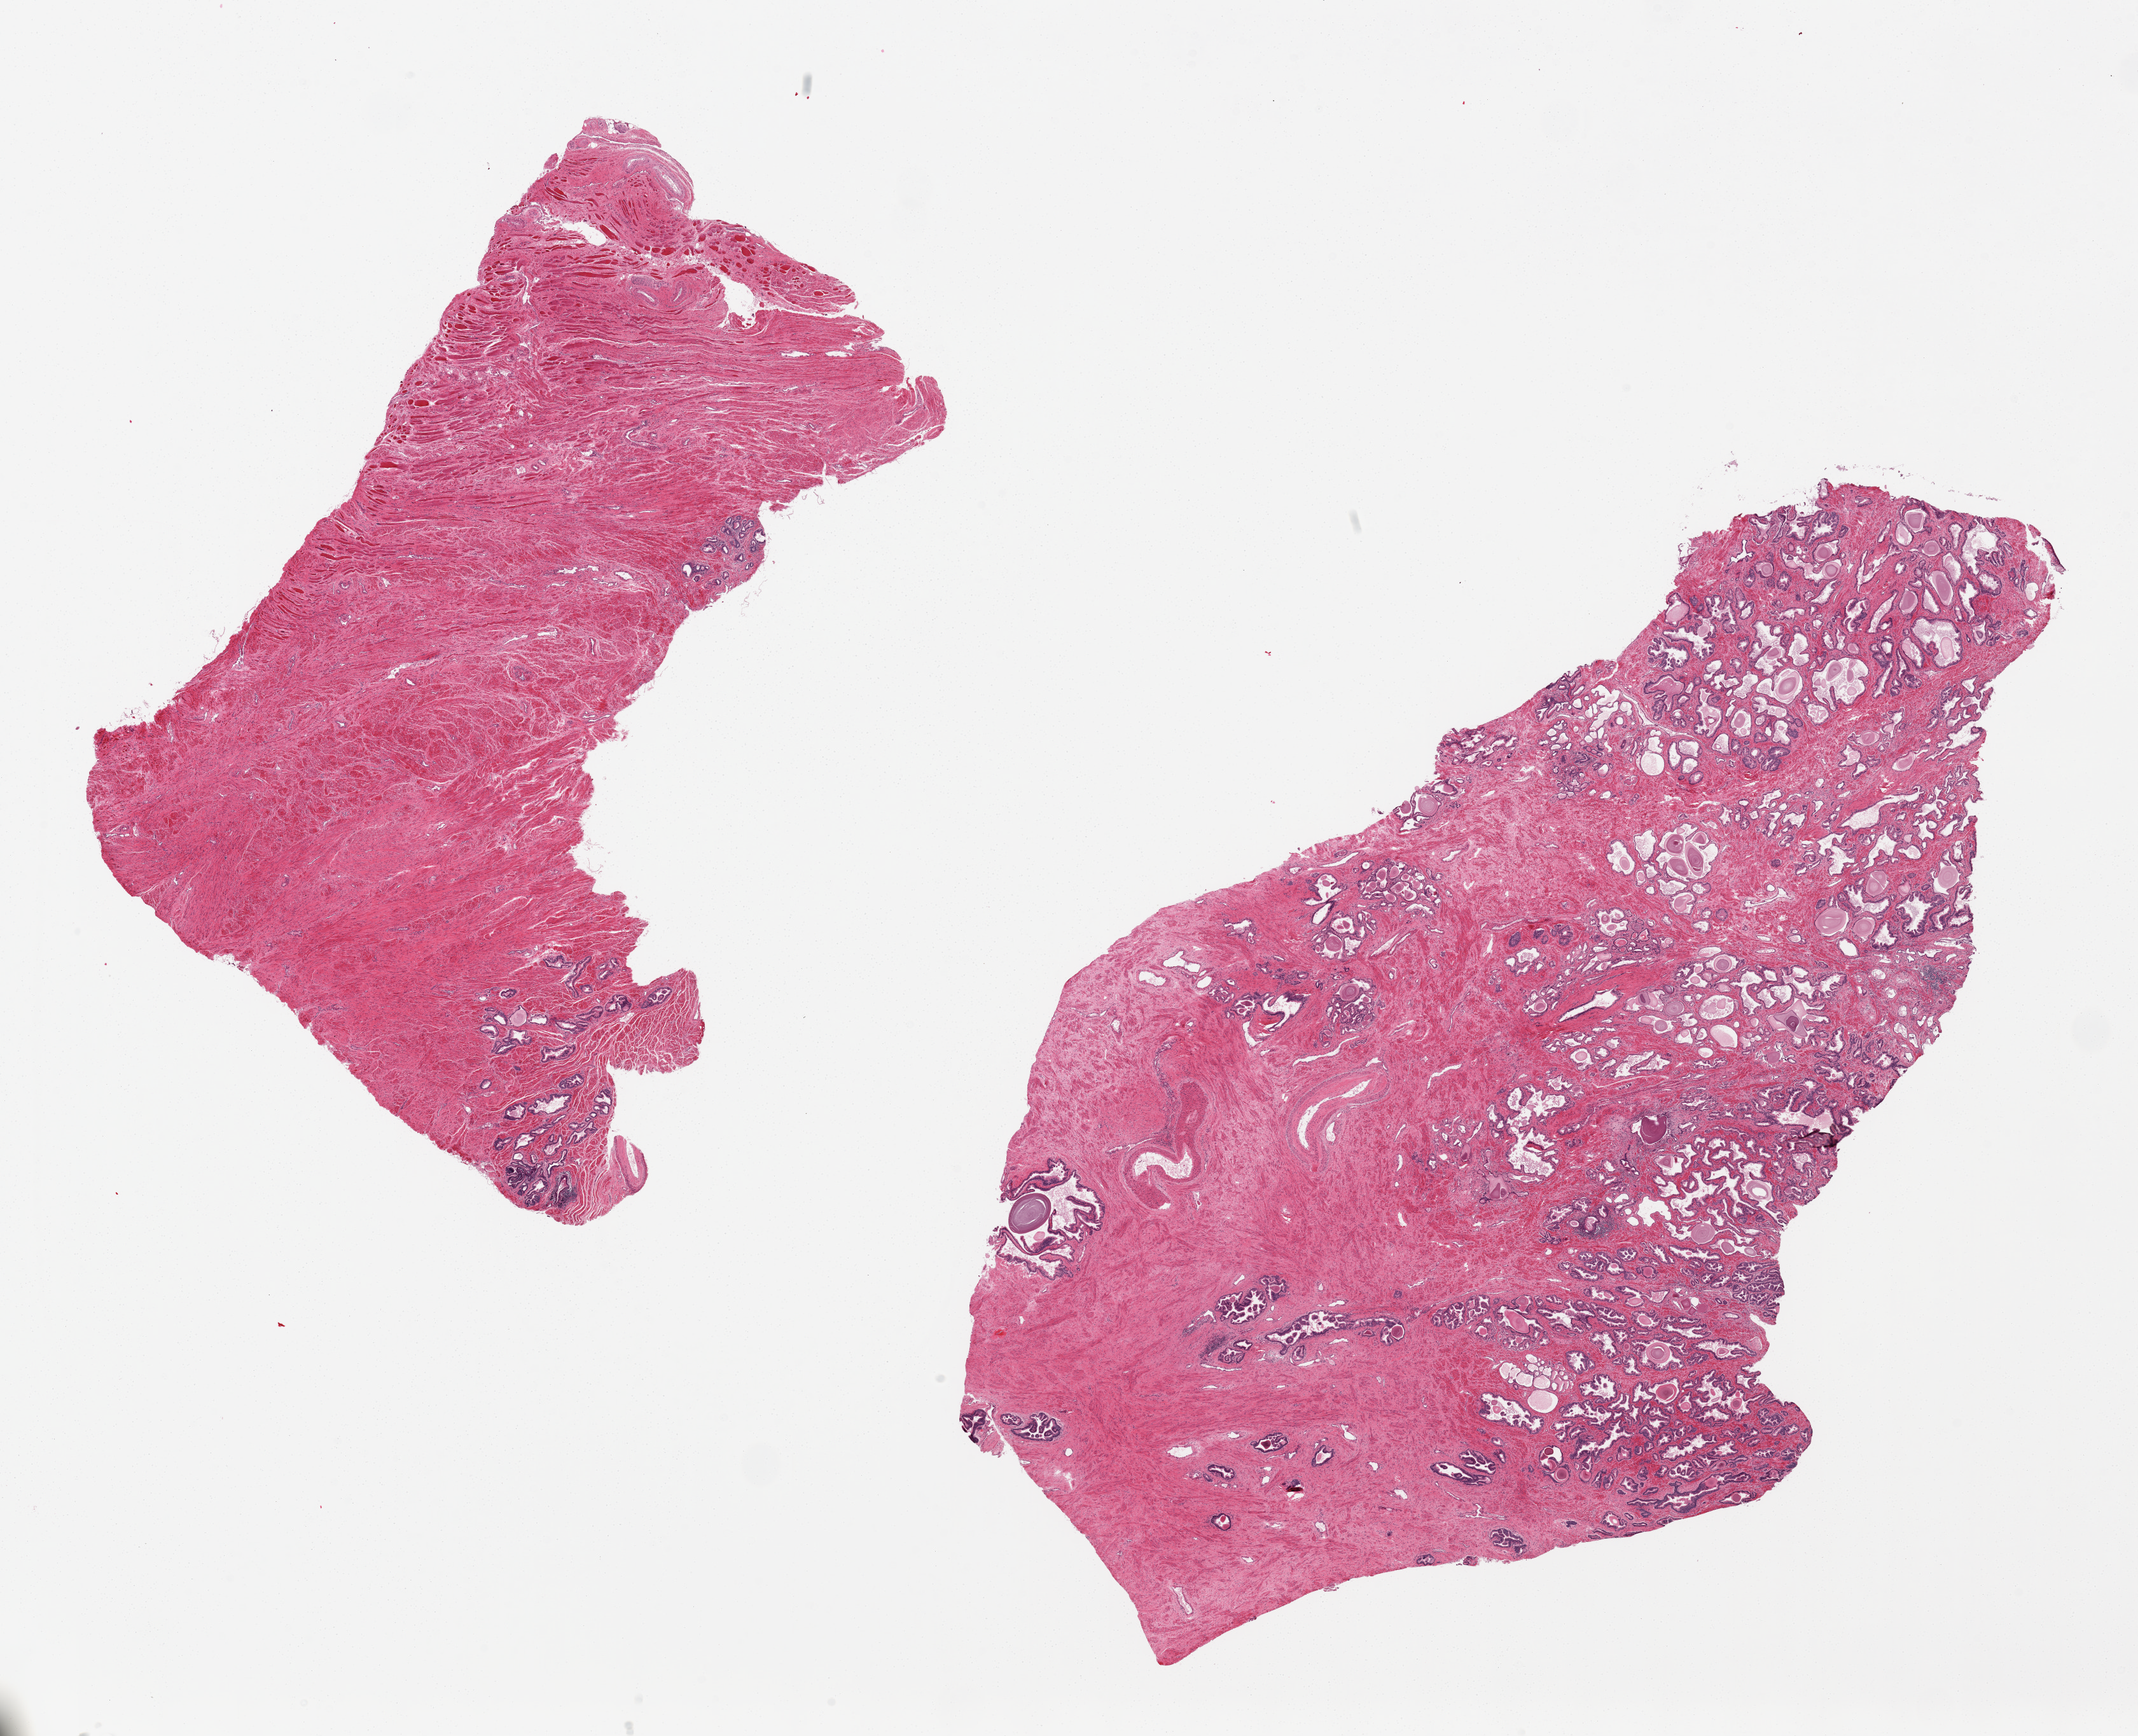
Whole-slide image, H&E stain, brightfield — a low-resolution overview of the entire scanned area, about 26.6 x 21.6 mm, PAXgene-fixed paraffin-embedded (PFPE) section, section of prostate (target tissue), donor tissue sample. Male donor.
Review note (as recorded): 2 pieces; few foci of chronic inflammation; glands cover ~50% of the total specimen.